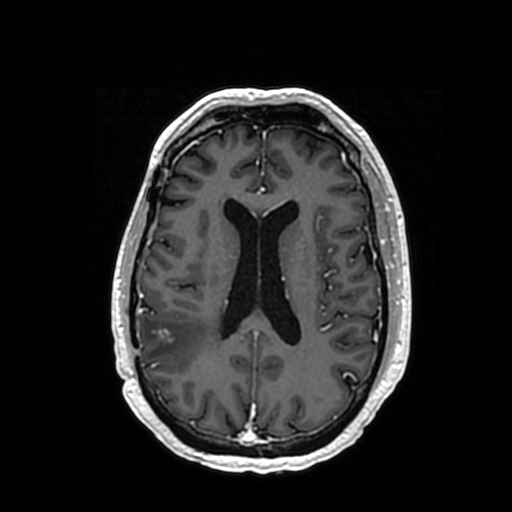
Brain MRI from a brain-tumour surgery series, one axial slice. Slice 151 of 364 in the series (ordered by position). T1-weighted post-contrast. 0.5 mm slice thickness. 512 × 512 image matrix, field of view 260 × 260 mm. From the clinical record (not read from this slice): histopathology: Oligodendroglioma; WHO grade: 3; IDH mutation: yes; tumour location: Right Posterior Temporal Inferior Parietal.
Annotated regions visible in this slice (expert manual segmentation):
- tumour: box from (x=161, y=330) to (x=169, y=337) px